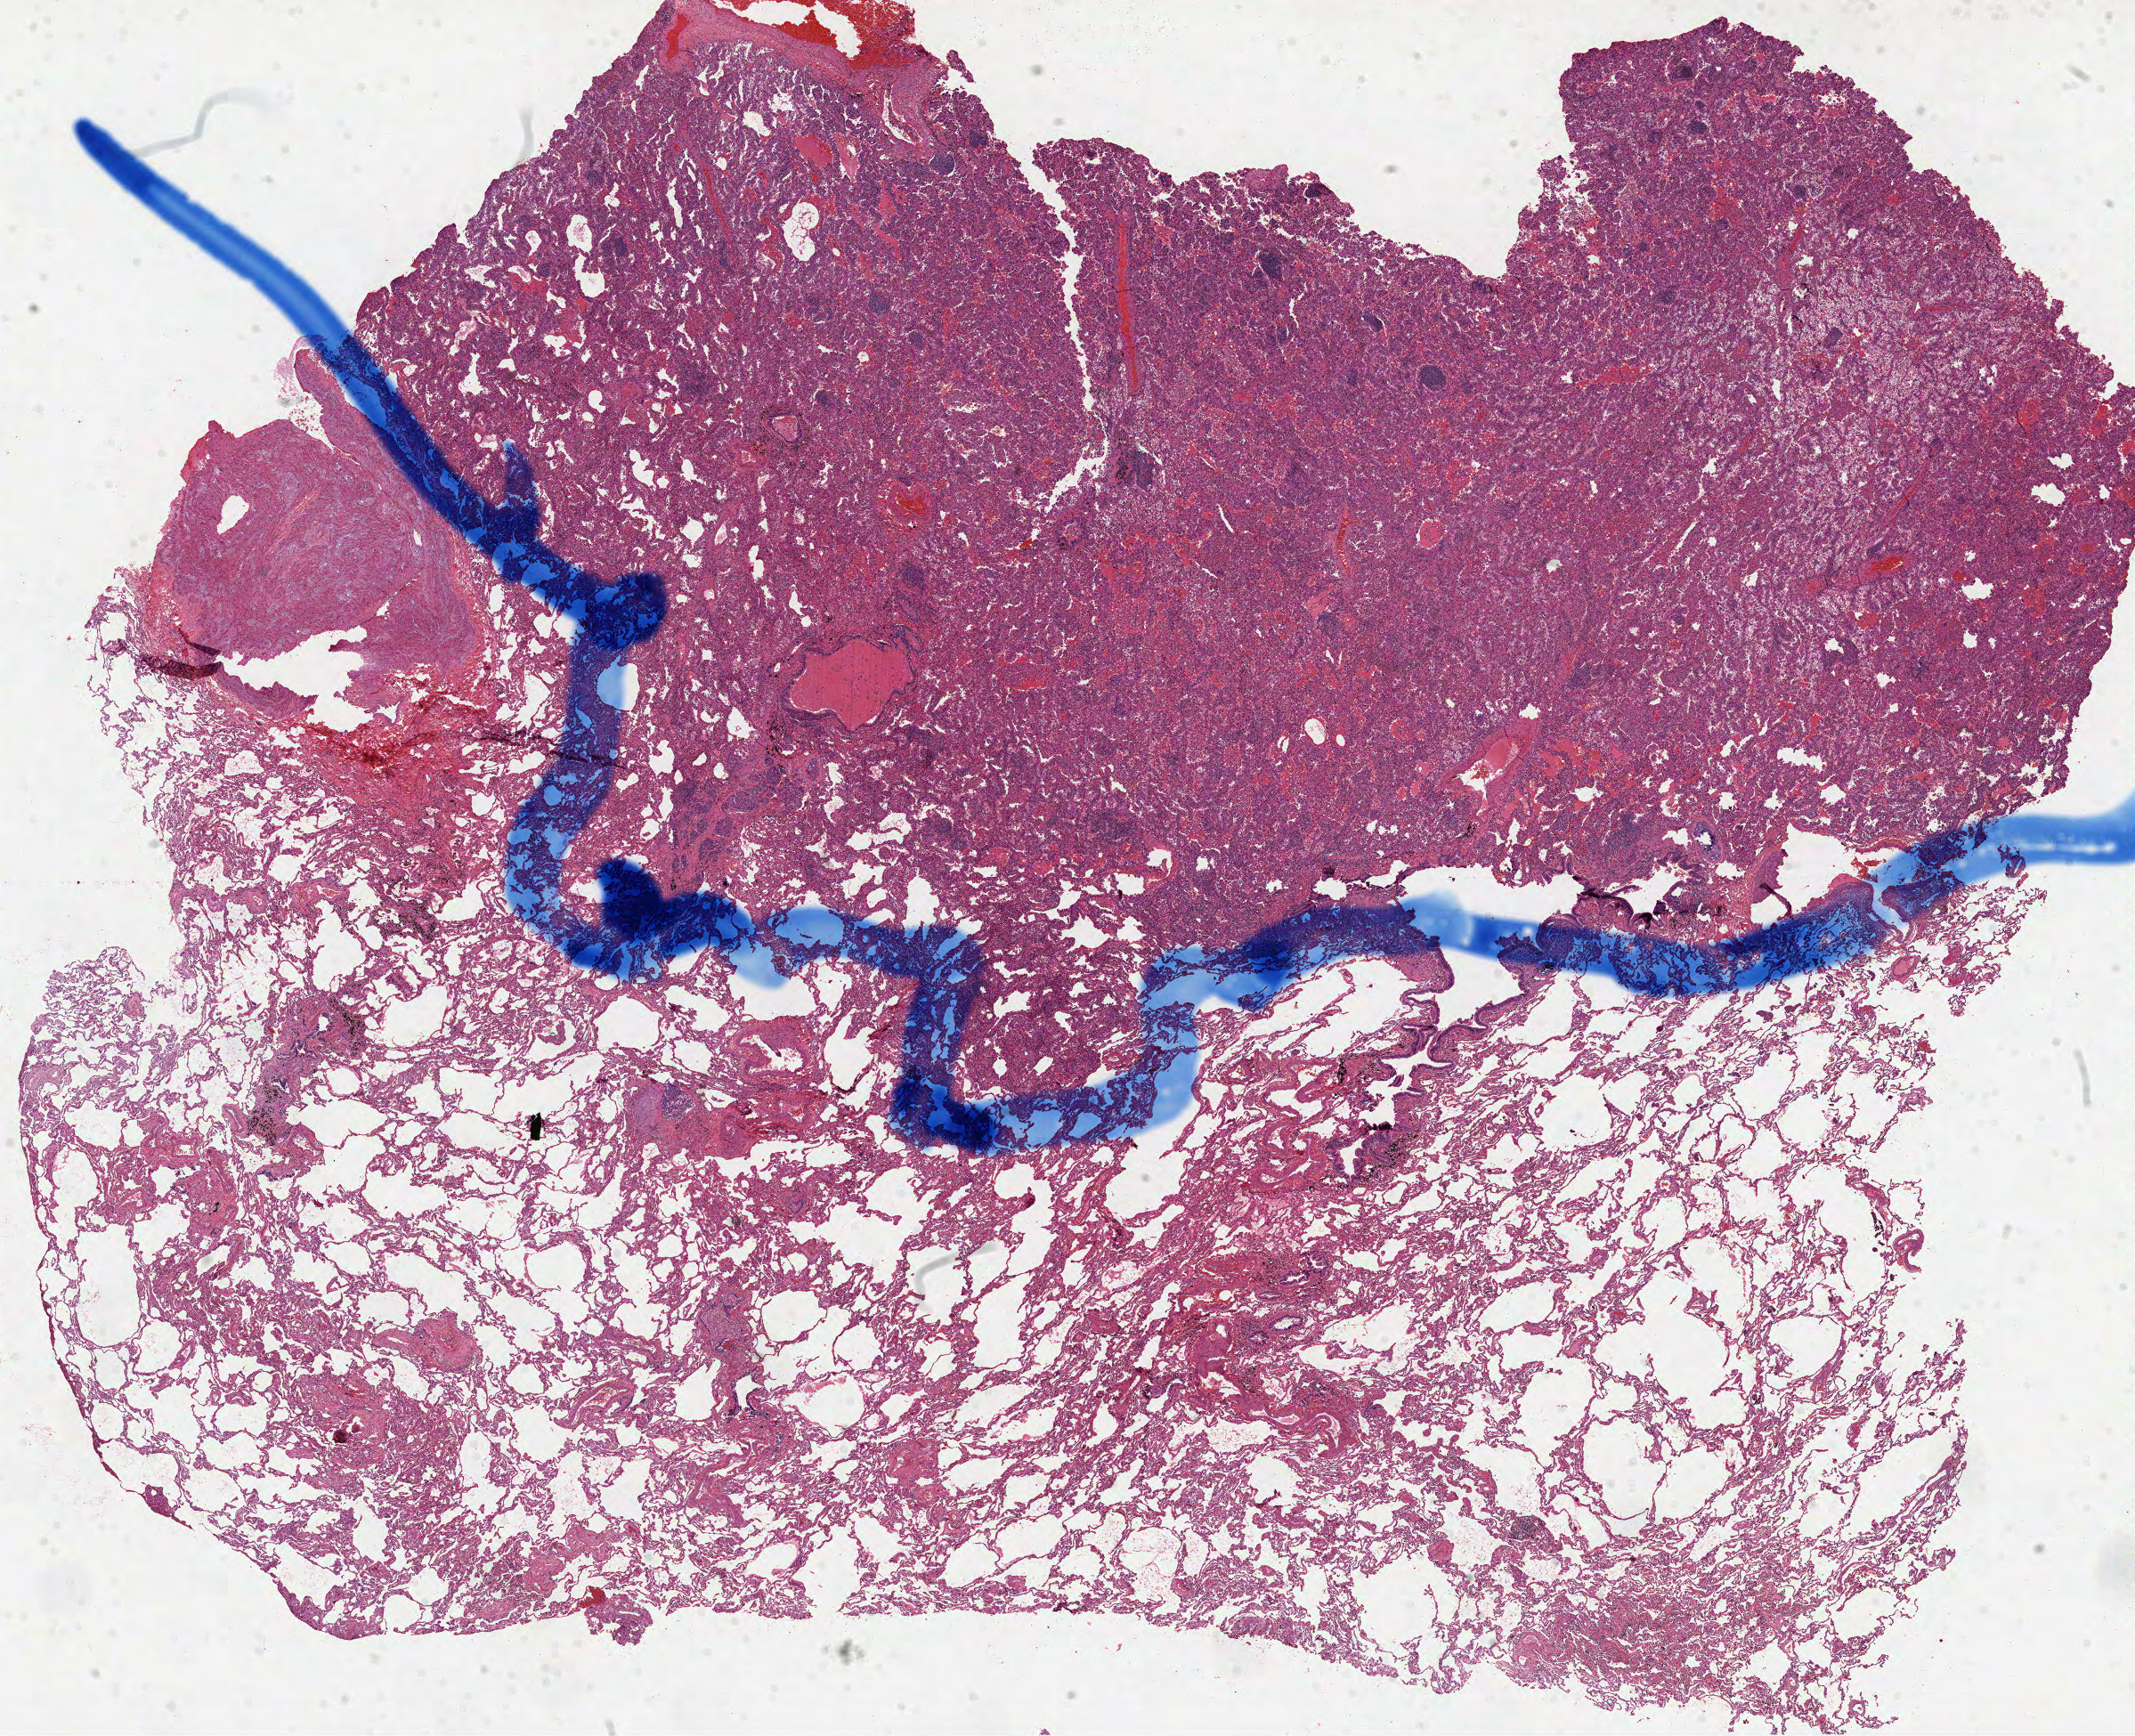
Digitized H&E tissue section (whole slide) — whole scanned area (about 19.3 x 15.7 mm, acquisition: 40x scan) shown as a low-resolution overview. FFPE section. Lung, primary tumour sample. Female patient; age at initial diagnosis 79 years.
Pathologic diagnosis: Adenocarcinoma, NOS (lower lobe, lung).